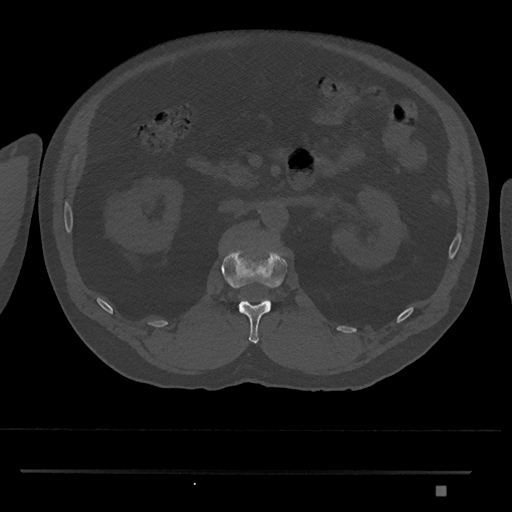
CT including the spine, one axial slice. Position 805 of 1134 along the scan axis. Reconstruction kernel Br40s/3. 120 kVp. Bone window (W 1800 / L 400 HU). 512 × 512 image matrix, field of view 429 × 429 mm. Male patient, age 65 years. From the clinical record (not read from this slice): primary cancer: prostate.
Structures marked on this image (semi-automatically segmented with operator editing):
- L1 vertebra: bounding box <220,249,288,344> (left, top, right, bottom; pixels)